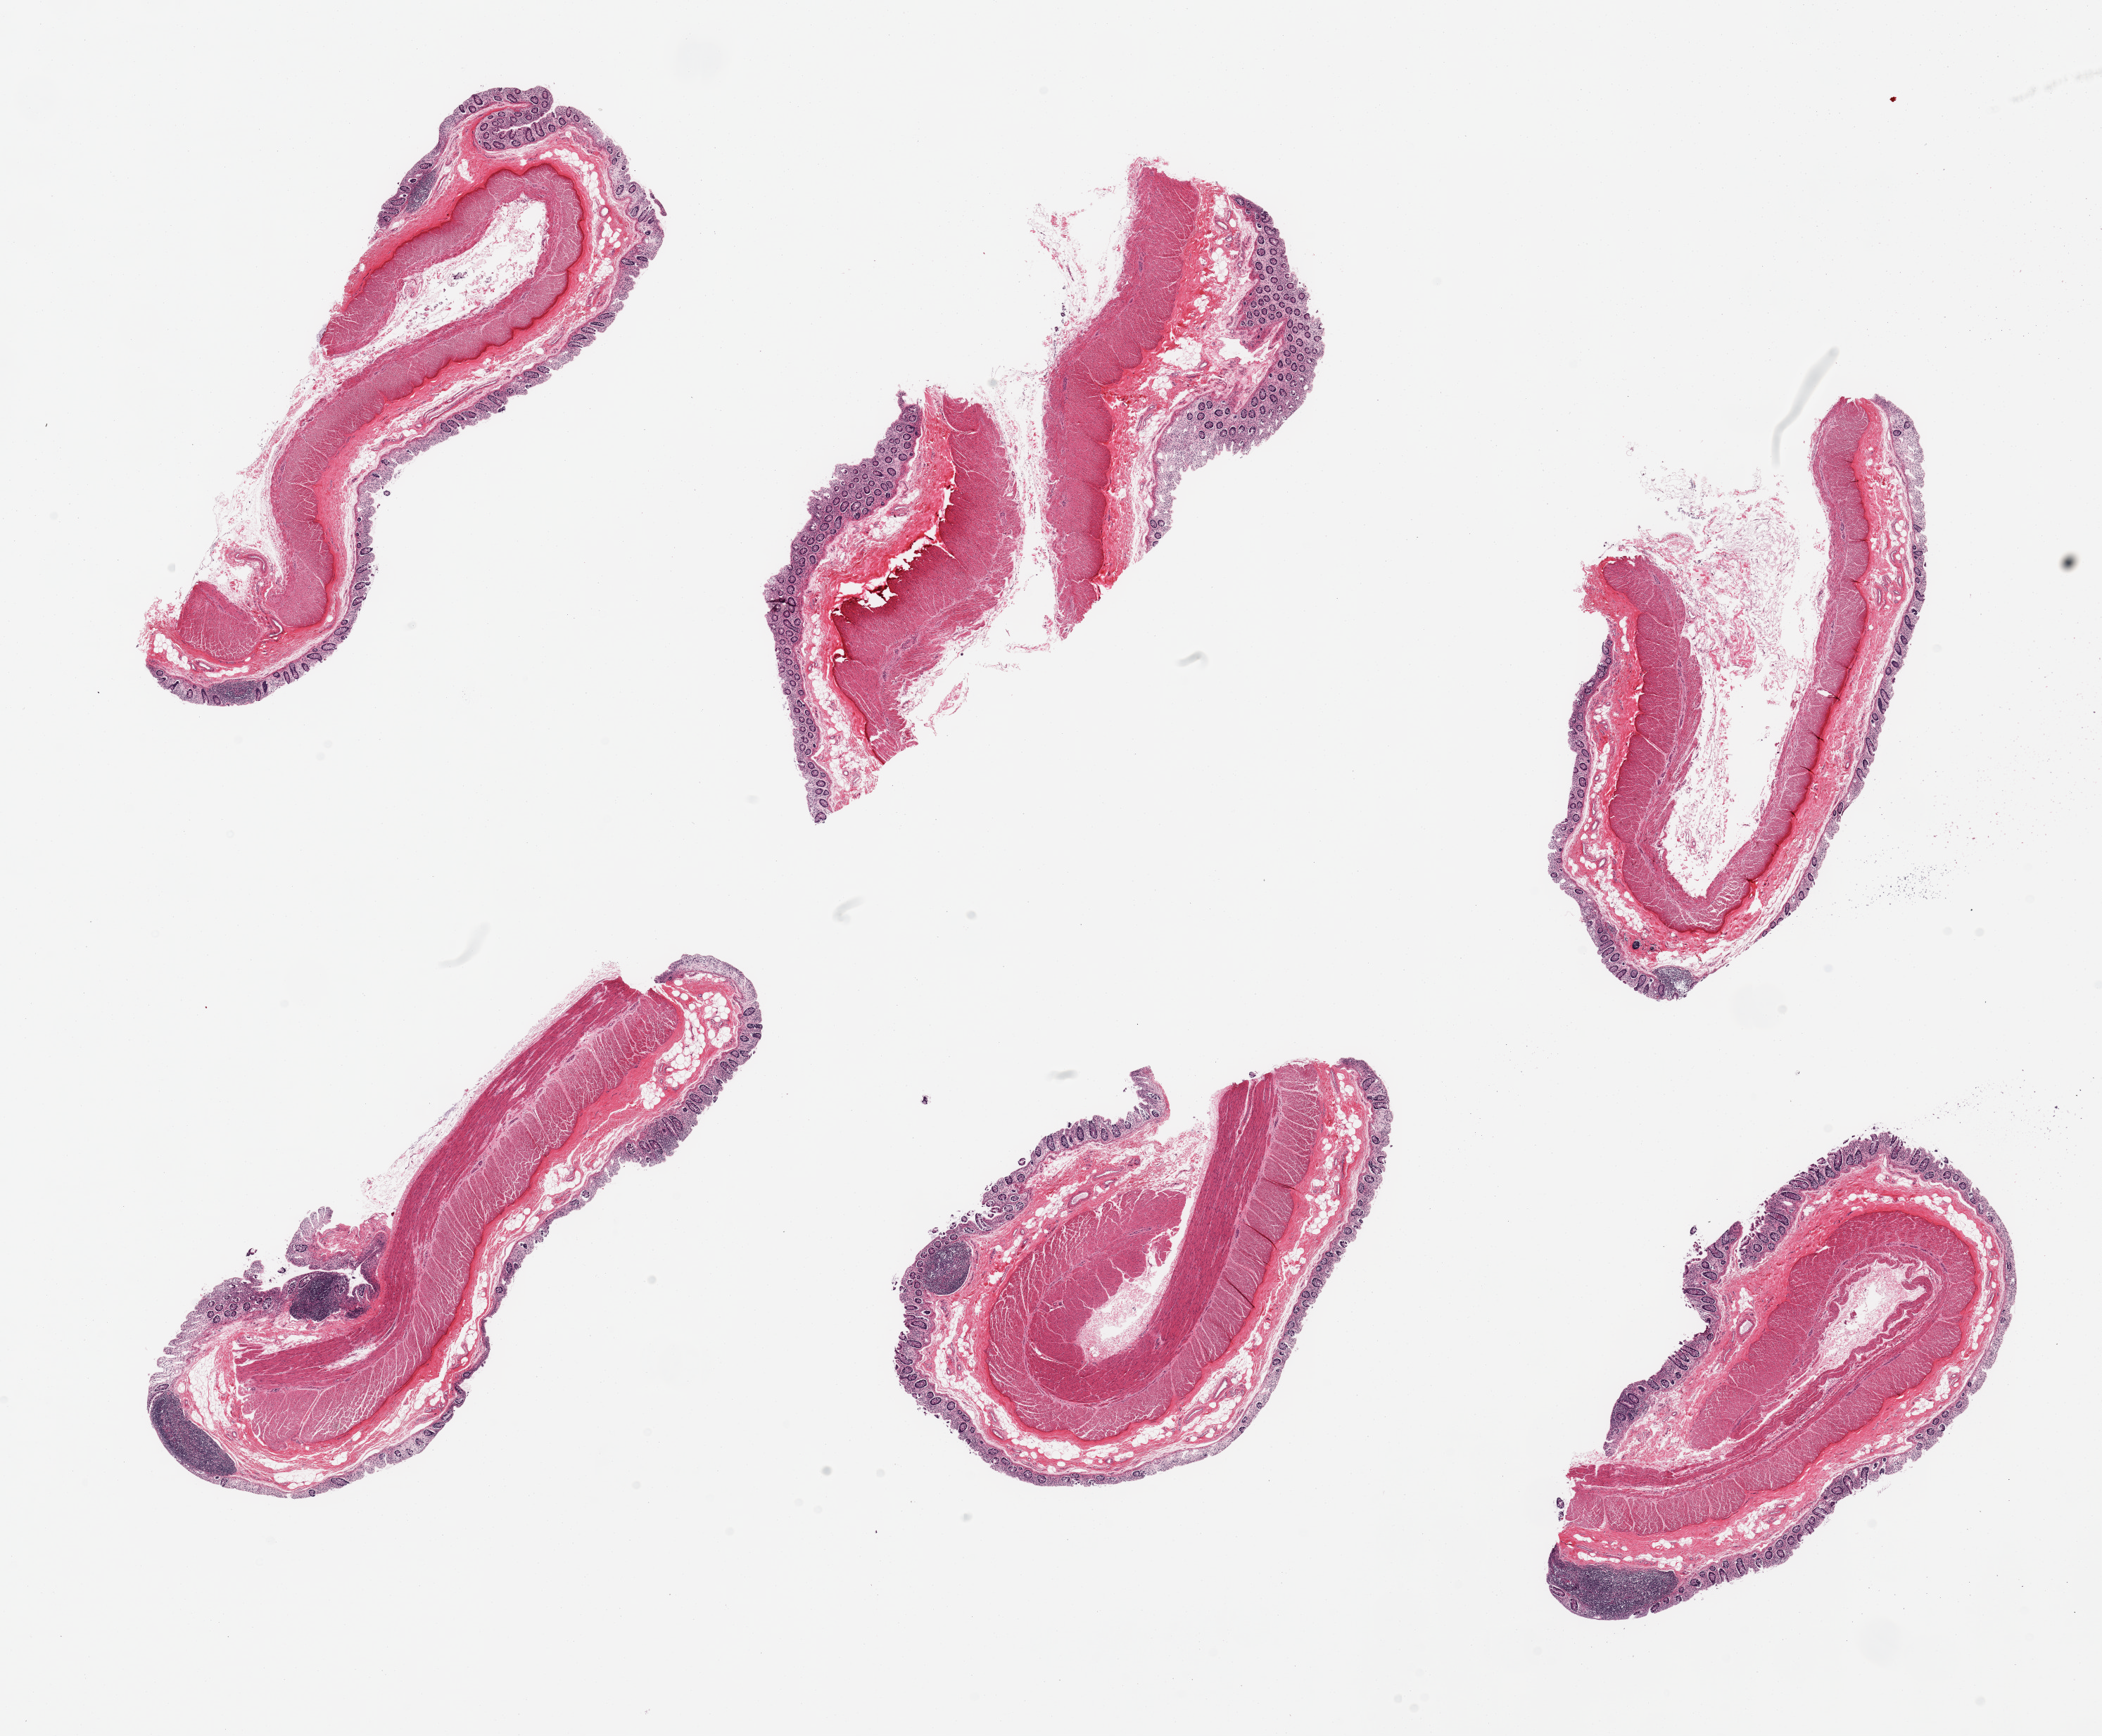
Digitized H&E-stained section, whole scanned area (about 23.6 x 19.5 mm, slide scanned at 20x) shown as a low-resolution overview. PAXgene-fixed, paraffin-embedded tissue. Section of transverse colon (target tissue). Tissue donor sample. Donor: male.
- review note (as recorded): 6 pieces